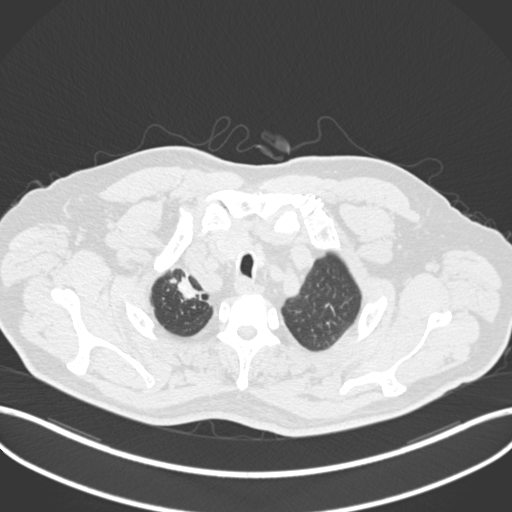
Chest CT, one axial slice; position 184 of 255 along the scan axis; reconstruction kernel B30f; 120 kVp; lung window (W 1500 / L -600 HU); 512 × 512 image matrix, field of view 400 × 400 mm. Male patient, age 60 years. Case-level facts recorded for this patient, not image findings: clinical TNM (as recorded): T1b N1 M0.
Structures marked on this image (bounding box drawn by a radiologist):
- lung tumour (recorded histology: squamous cell carcinoma): bounding box <172,271,206,309> (left, top, right, bottom; pixels)